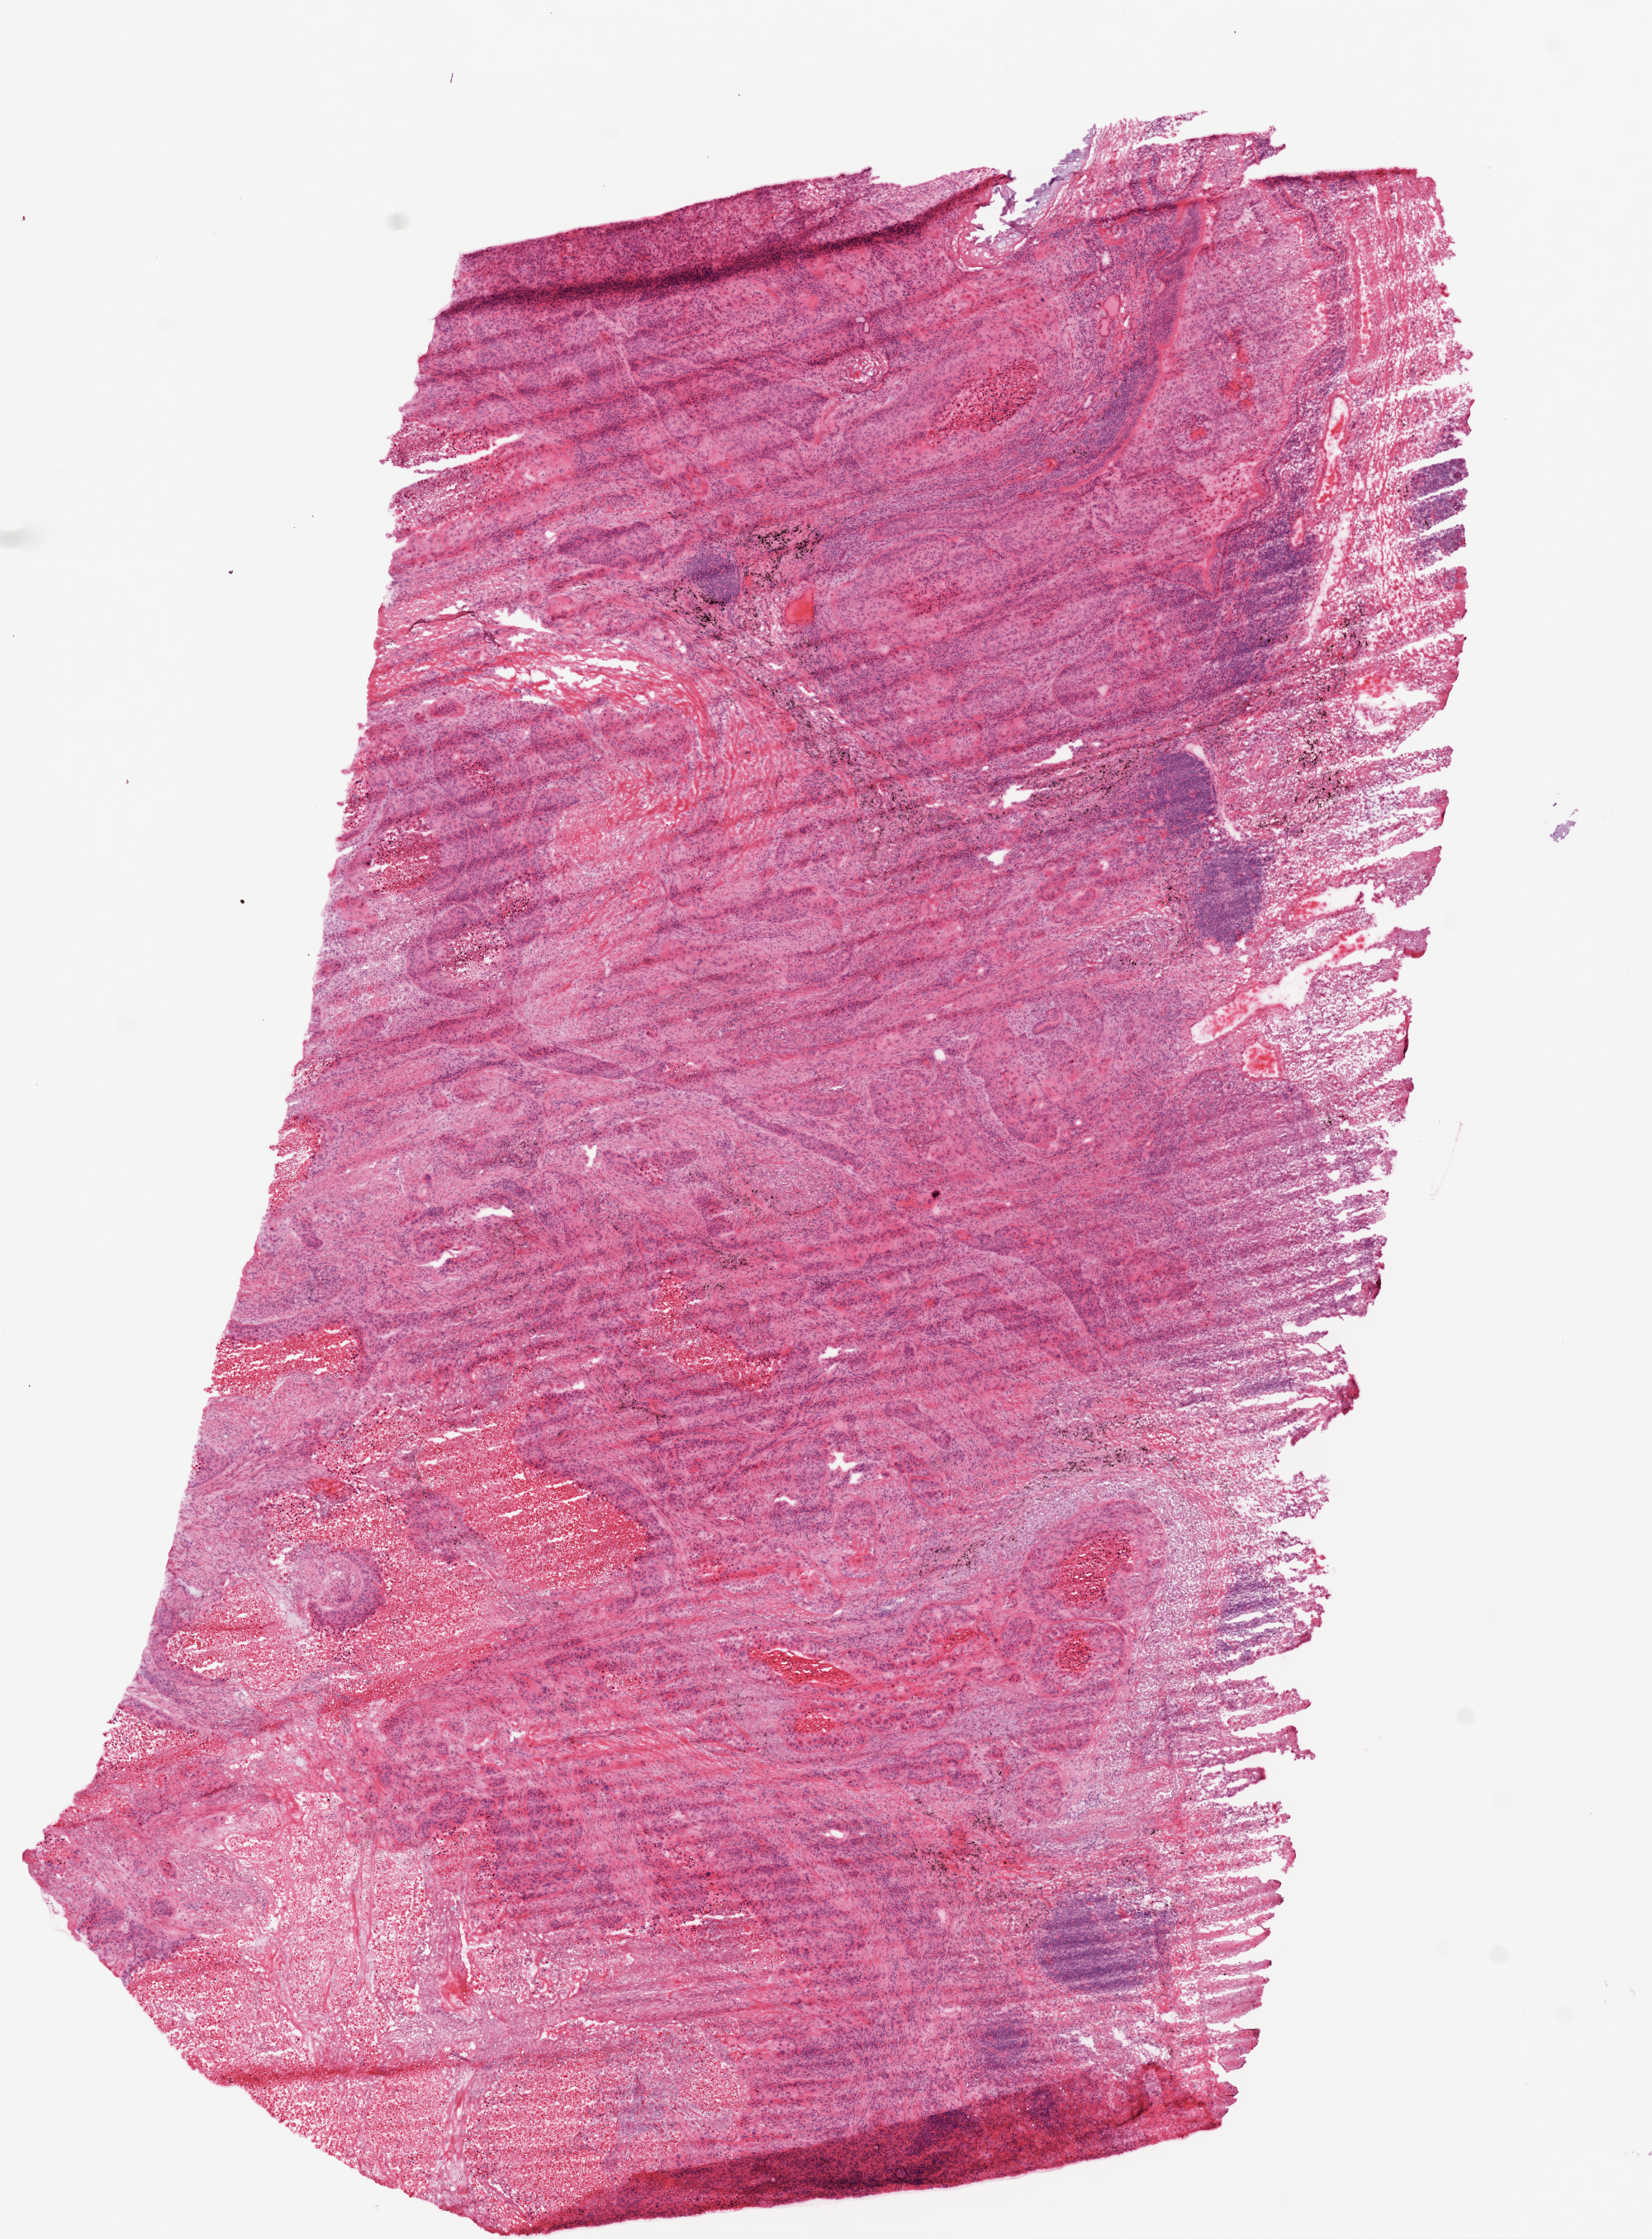
Whole-slide histology image, Hematoxylin and eosin (H&E) stained, shown as a low-resolution overview of the whole scanned area (about 8.0 x 10.9 mm, from a 20x scan), frozen section, sample: primary tumour, lung. Male, age 79 years at initial diagnosis. Composition of this section per pathologist review: tumour cells 55%, tumour nuclei 60%, normal cells 5%, stromal cells 20%, necrosis 20%. Inflammatory infiltration, as recorded: lymphocyte infiltration 15%, monocyte infiltration 0%, neutrophil infiltration 0%.
AJCC pathologic stage: IB. Diagnosis: Squamous cell carcinoma, NOS (lower lobe, lung). Laterality: right.